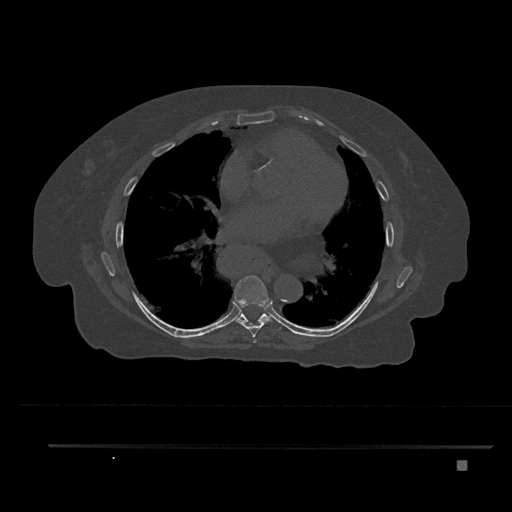
CT including the spine, one axial slice; 120 kVp; bone window (W 1800 / L 400 HU); 0.5 mm slice thickness; 512 × 512 image matrix. Female patient, age 76 years. From the clinical record (not read from this slice): primary cancer: lung; vertebrae with lytic lesions (as recorded): T11, L3.
Annotated regions visible in this slice (semi-automatic segmentation, software-assisted and operator-edited):
- T6 vertebra: box from (x=253, y=339) to (x=257, y=343) px
- T7 vertebra: (x=234, y=275)–(x=272, y=337)
- T8 vertebra: (x=237, y=313)–(x=271, y=322)